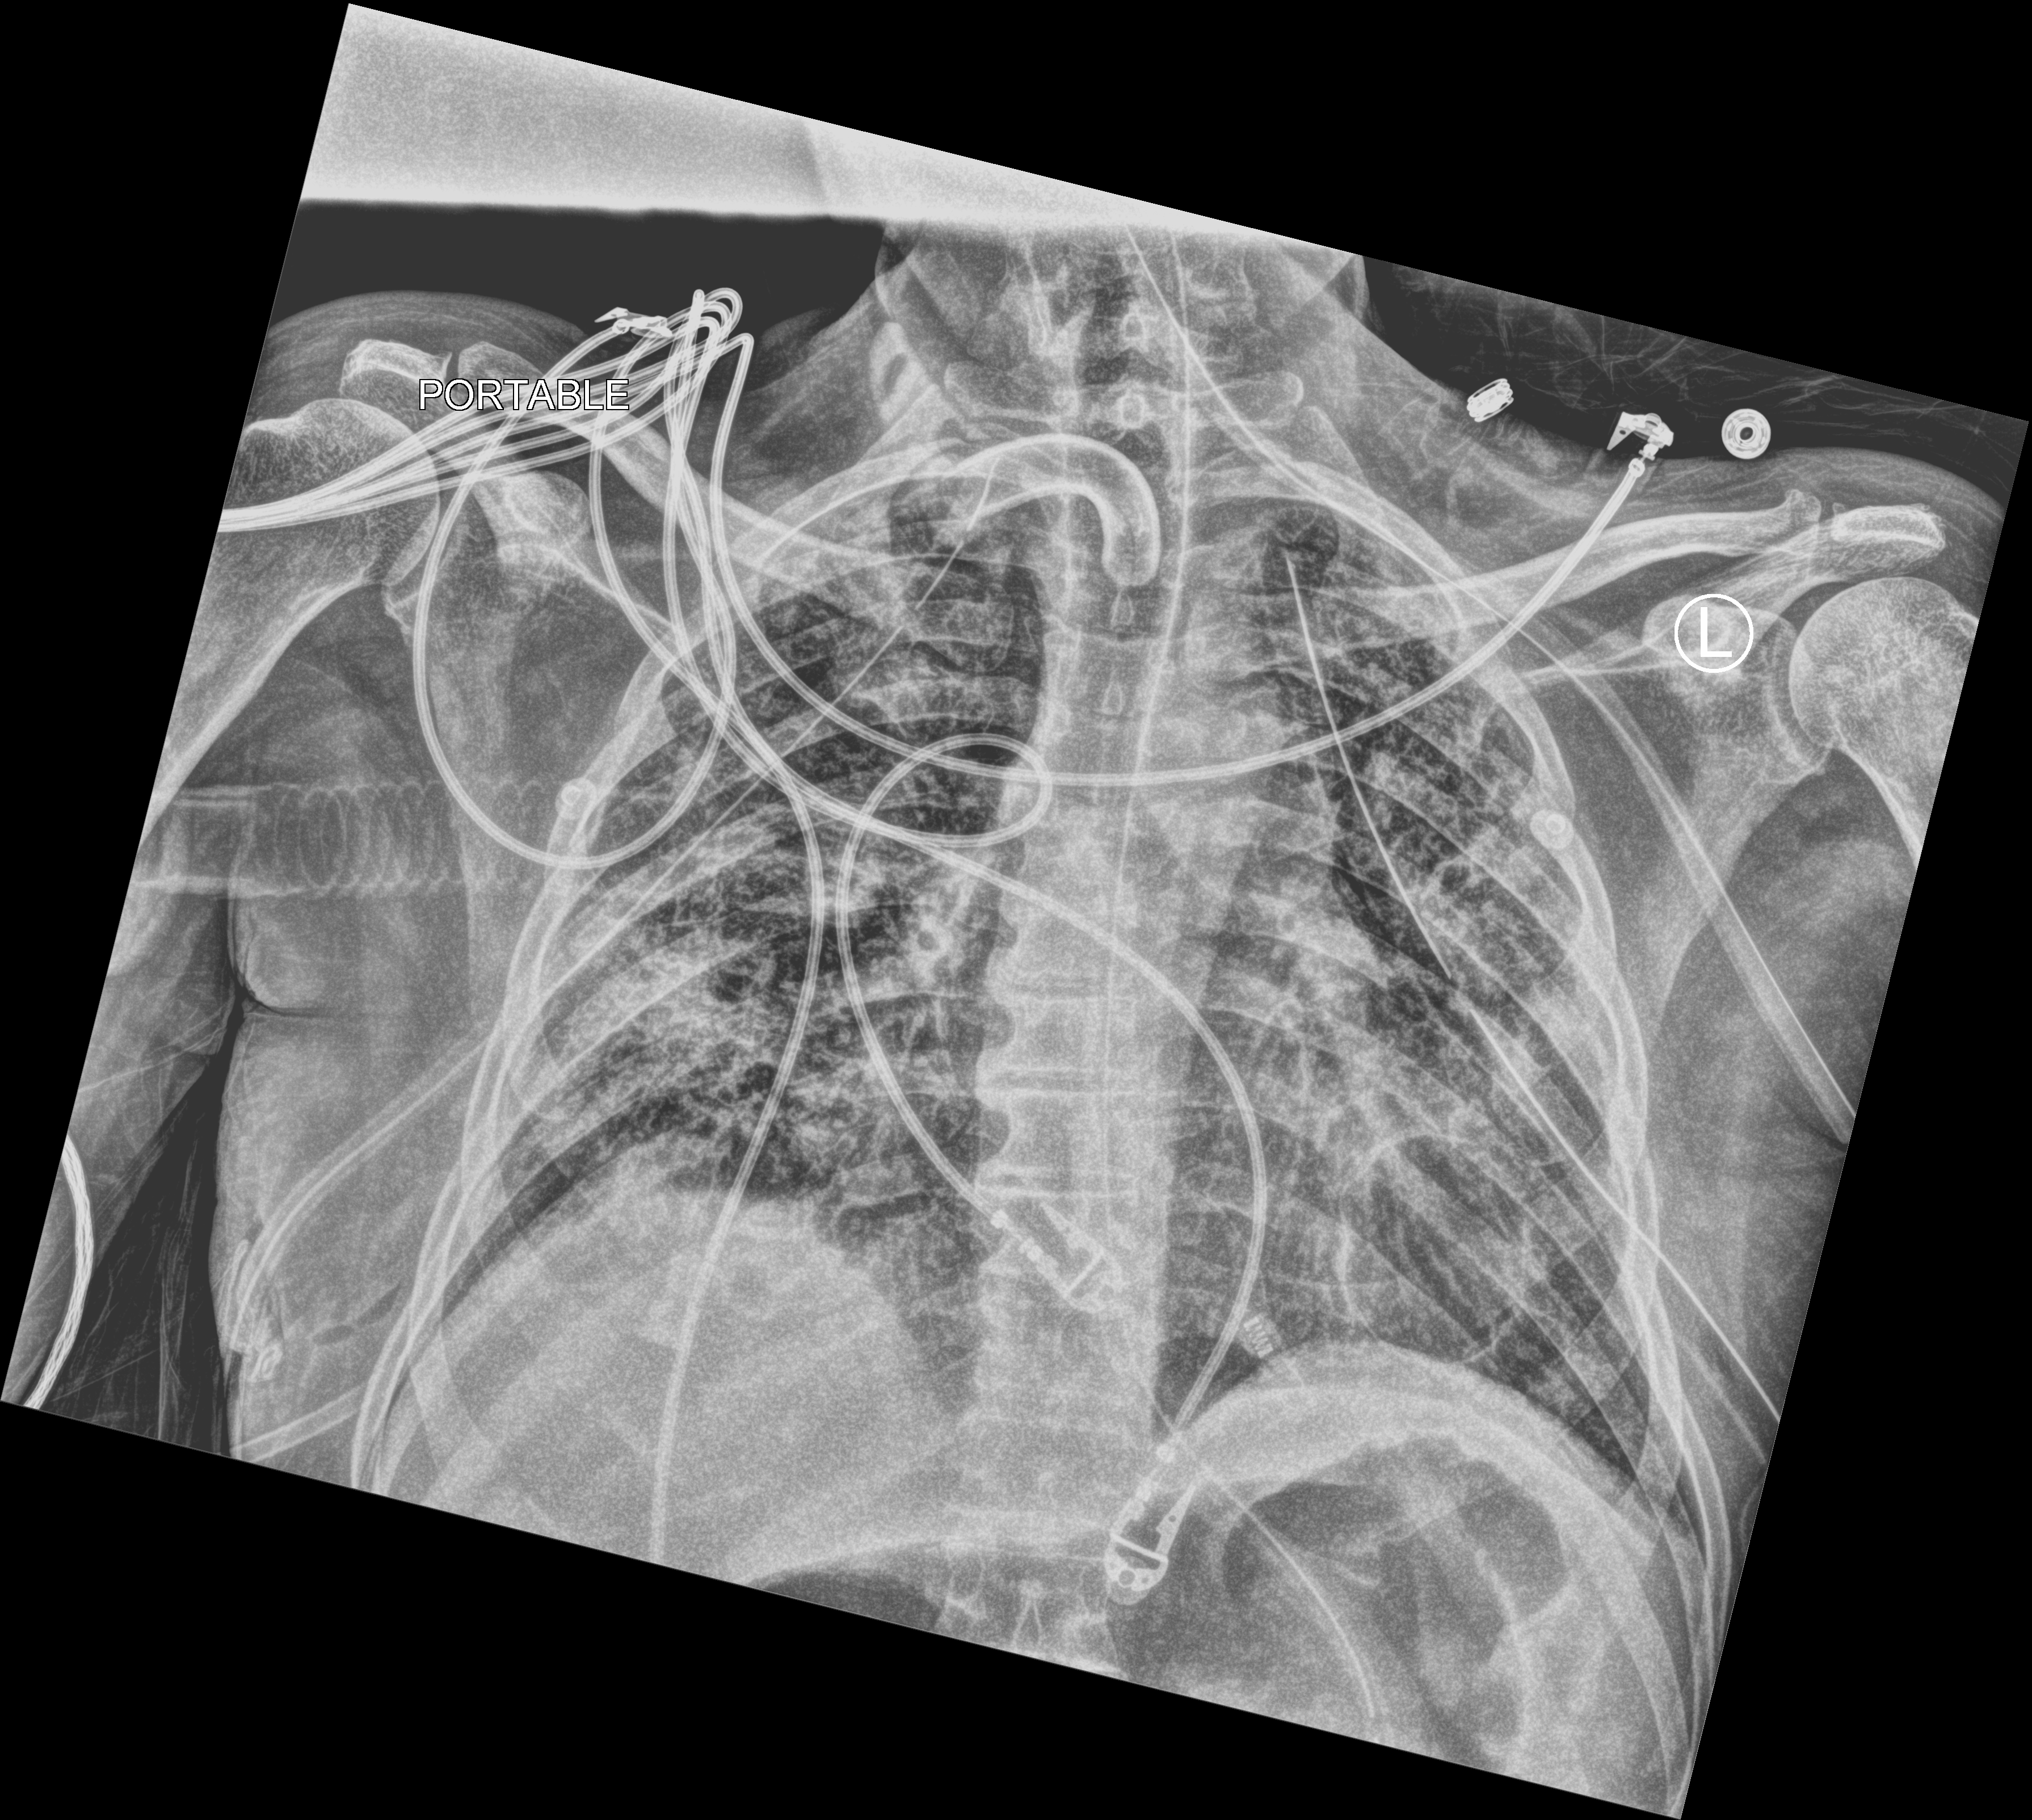
Chest X-ray (portable), anteroposterior (AP) projection. Patient hospitalised with COVID-19; male, aged 18–59 years.
From the hospital-stay record, not from the radiograph (when in the stay this image was taken is not recorded):
- other chronic lung disease (admission record): no
- admitted to intensive care during this hospital stay: yes